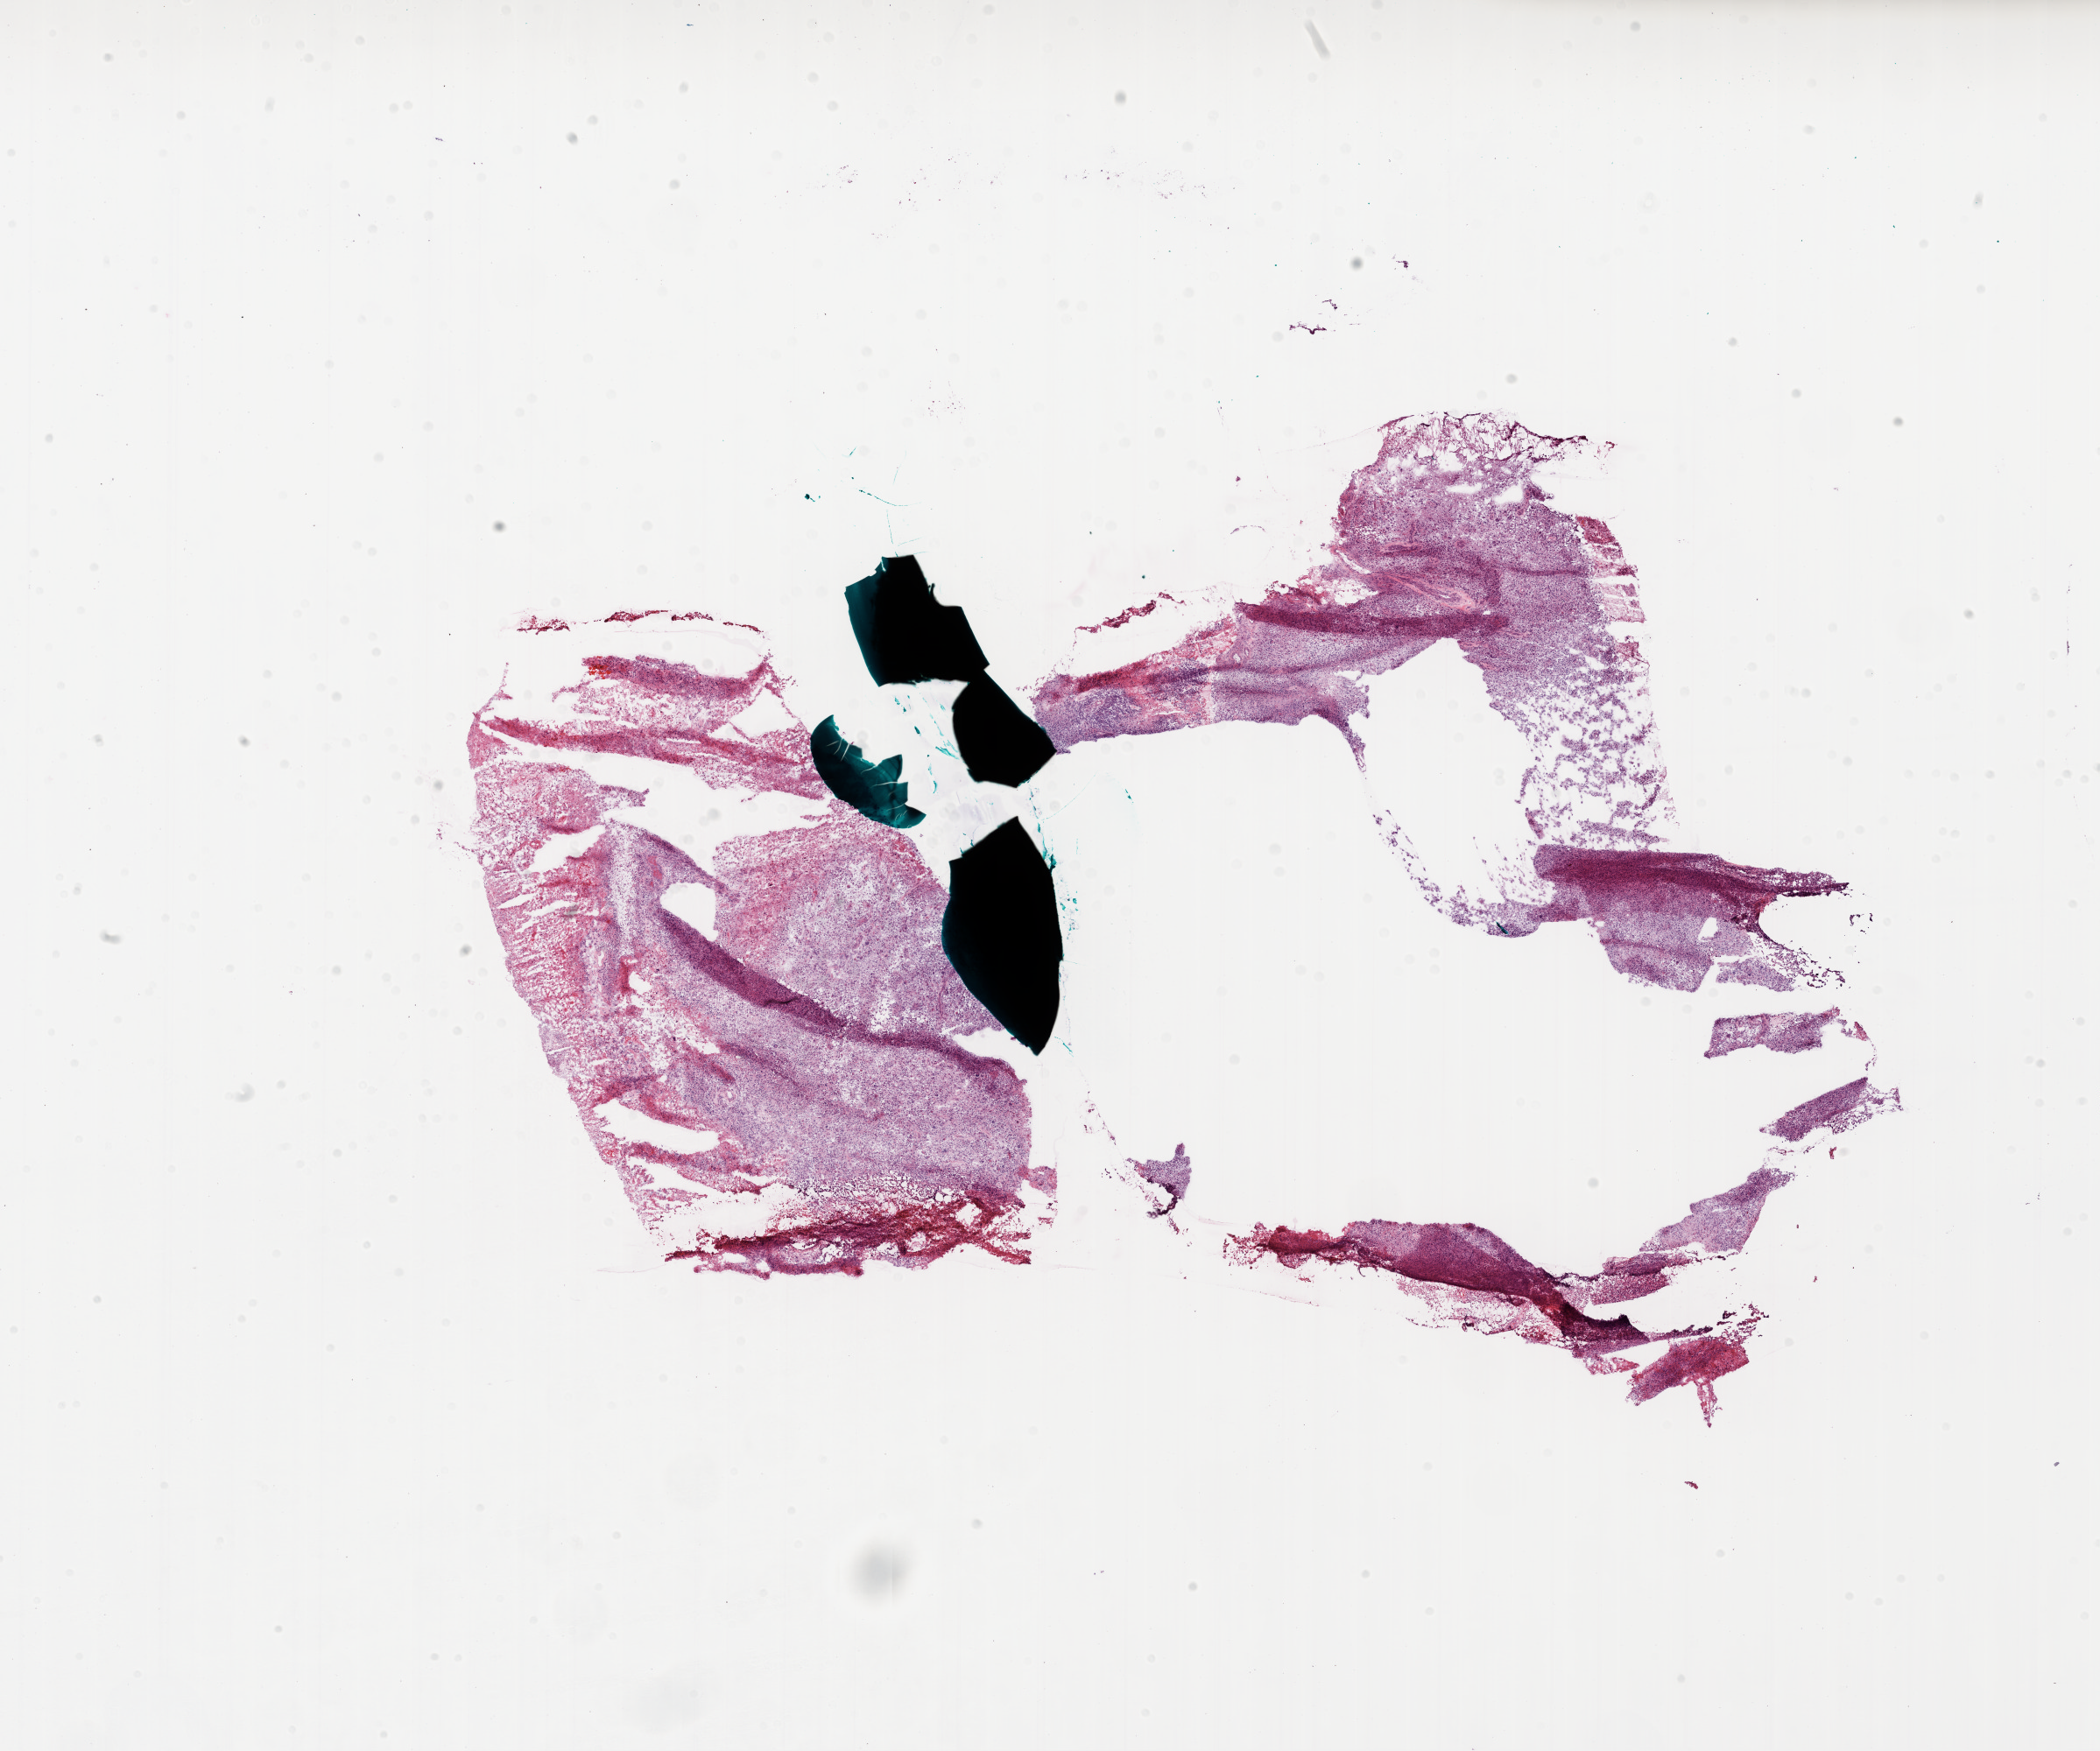
Whole-slide histology image, H&E, a low-resolution overview of the entire scanned area, about 19.3 x 16.1 mm (acquisition: 20x scan), frozen section from the bottom of the tissue portion, sample: primary tumour, brain. Male patient; age at initial diagnosis 67 years. Pathologist review of this section (percent, as recorded): tumour cells 80%, tumour nuclei 100%, normal cells 0%, stromal cells 0%, necrosis 20%.
Histologic diagnosis: Glioblastoma.